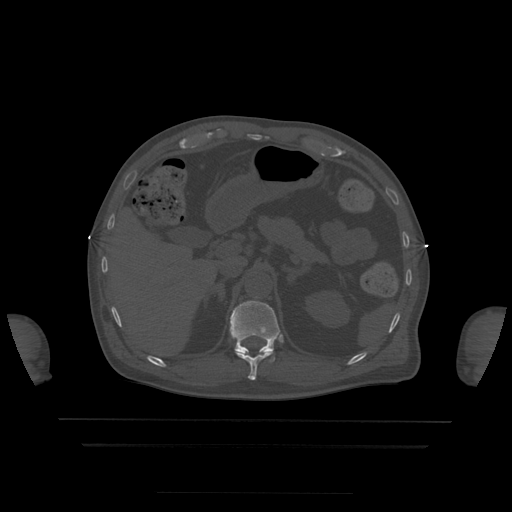
CT including the spine, one axial slice; slice 207 of 522 in the series (ordered by position); bone window (W 1800 / L 400 HU); 1.25 mm slice thickness; 512 × 512 image matrix. Patient age 68 years. From the clinical record (not read from this slice): primary cancer: urothelial.
Structures marked on this image (semi-automatic segmentation, software-assisted and operator-edited):
- T11 vertebra: bounding box (x1, y1, x2, y2) in pixels: (235, 351, 275, 380)
- T12 vertebra: (230, 300, 280, 354)